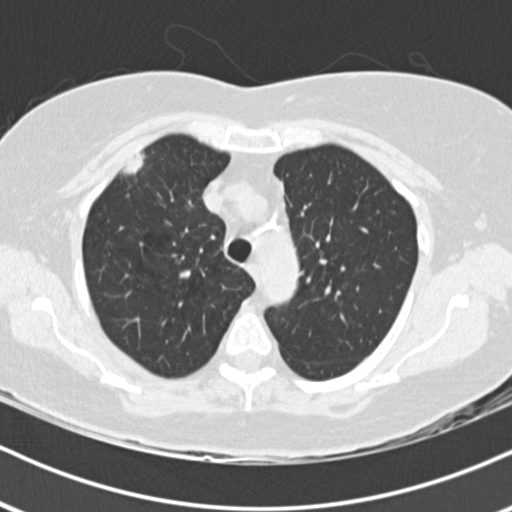
Low-dose screening chest CT, axial slice. Baseline screening round. Lung window (W 1500 / L -600 HU). 2 mm slice thickness. Standard (soft-tissue) reconstruction kernel (B30f). 512 × 512 image matrix. Female participant, aged 74 years at enrolment. Former smoker at enrolment.
• Expert-annotated lung lesion, box from (x=104, y=140) to (x=161, y=194) px.
• The exam's reader record, not a measurement of the box and not confirmed to be the same lesion: non-calcified nodule or mass ≥4 mm, right upper lobe, 16 × 10 mm, poorly defined margins, soft tissue attenuation.
• Official screen result: positive, change unspecified: nodule(s) >= 4 mm or enlarging nodule(s), mass(es), or other non-specific abnormalities suspicious for lung cancer.
• Lung cancer was diagnosed 33 days after this screen: adenocarcinoma, NOS, right upper lobe, poorly differentiated (G3), stage IIIA (AJCC 6th edition), 24 mm at pathology.